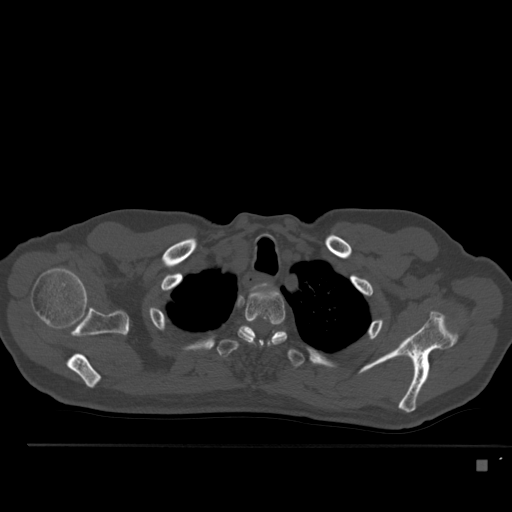
CT including the spine, one axial slice; slice 408 of 517 in the series (ordered by position); 120 kVp; bone window (W 1800 / L 400 HU); 512 × 512 image matrix. Patient: male, 70 years. From the clinical record (not read from this slice): primary cancer: renal.
Structures marked on this image (semi-automatic segmentation, software-assisted and operator-edited):
- T2 vertebra: box from (x=238, y=289) to (x=287, y=349) px
- T3 vertebra: (x=217, y=326)–(x=305, y=368)